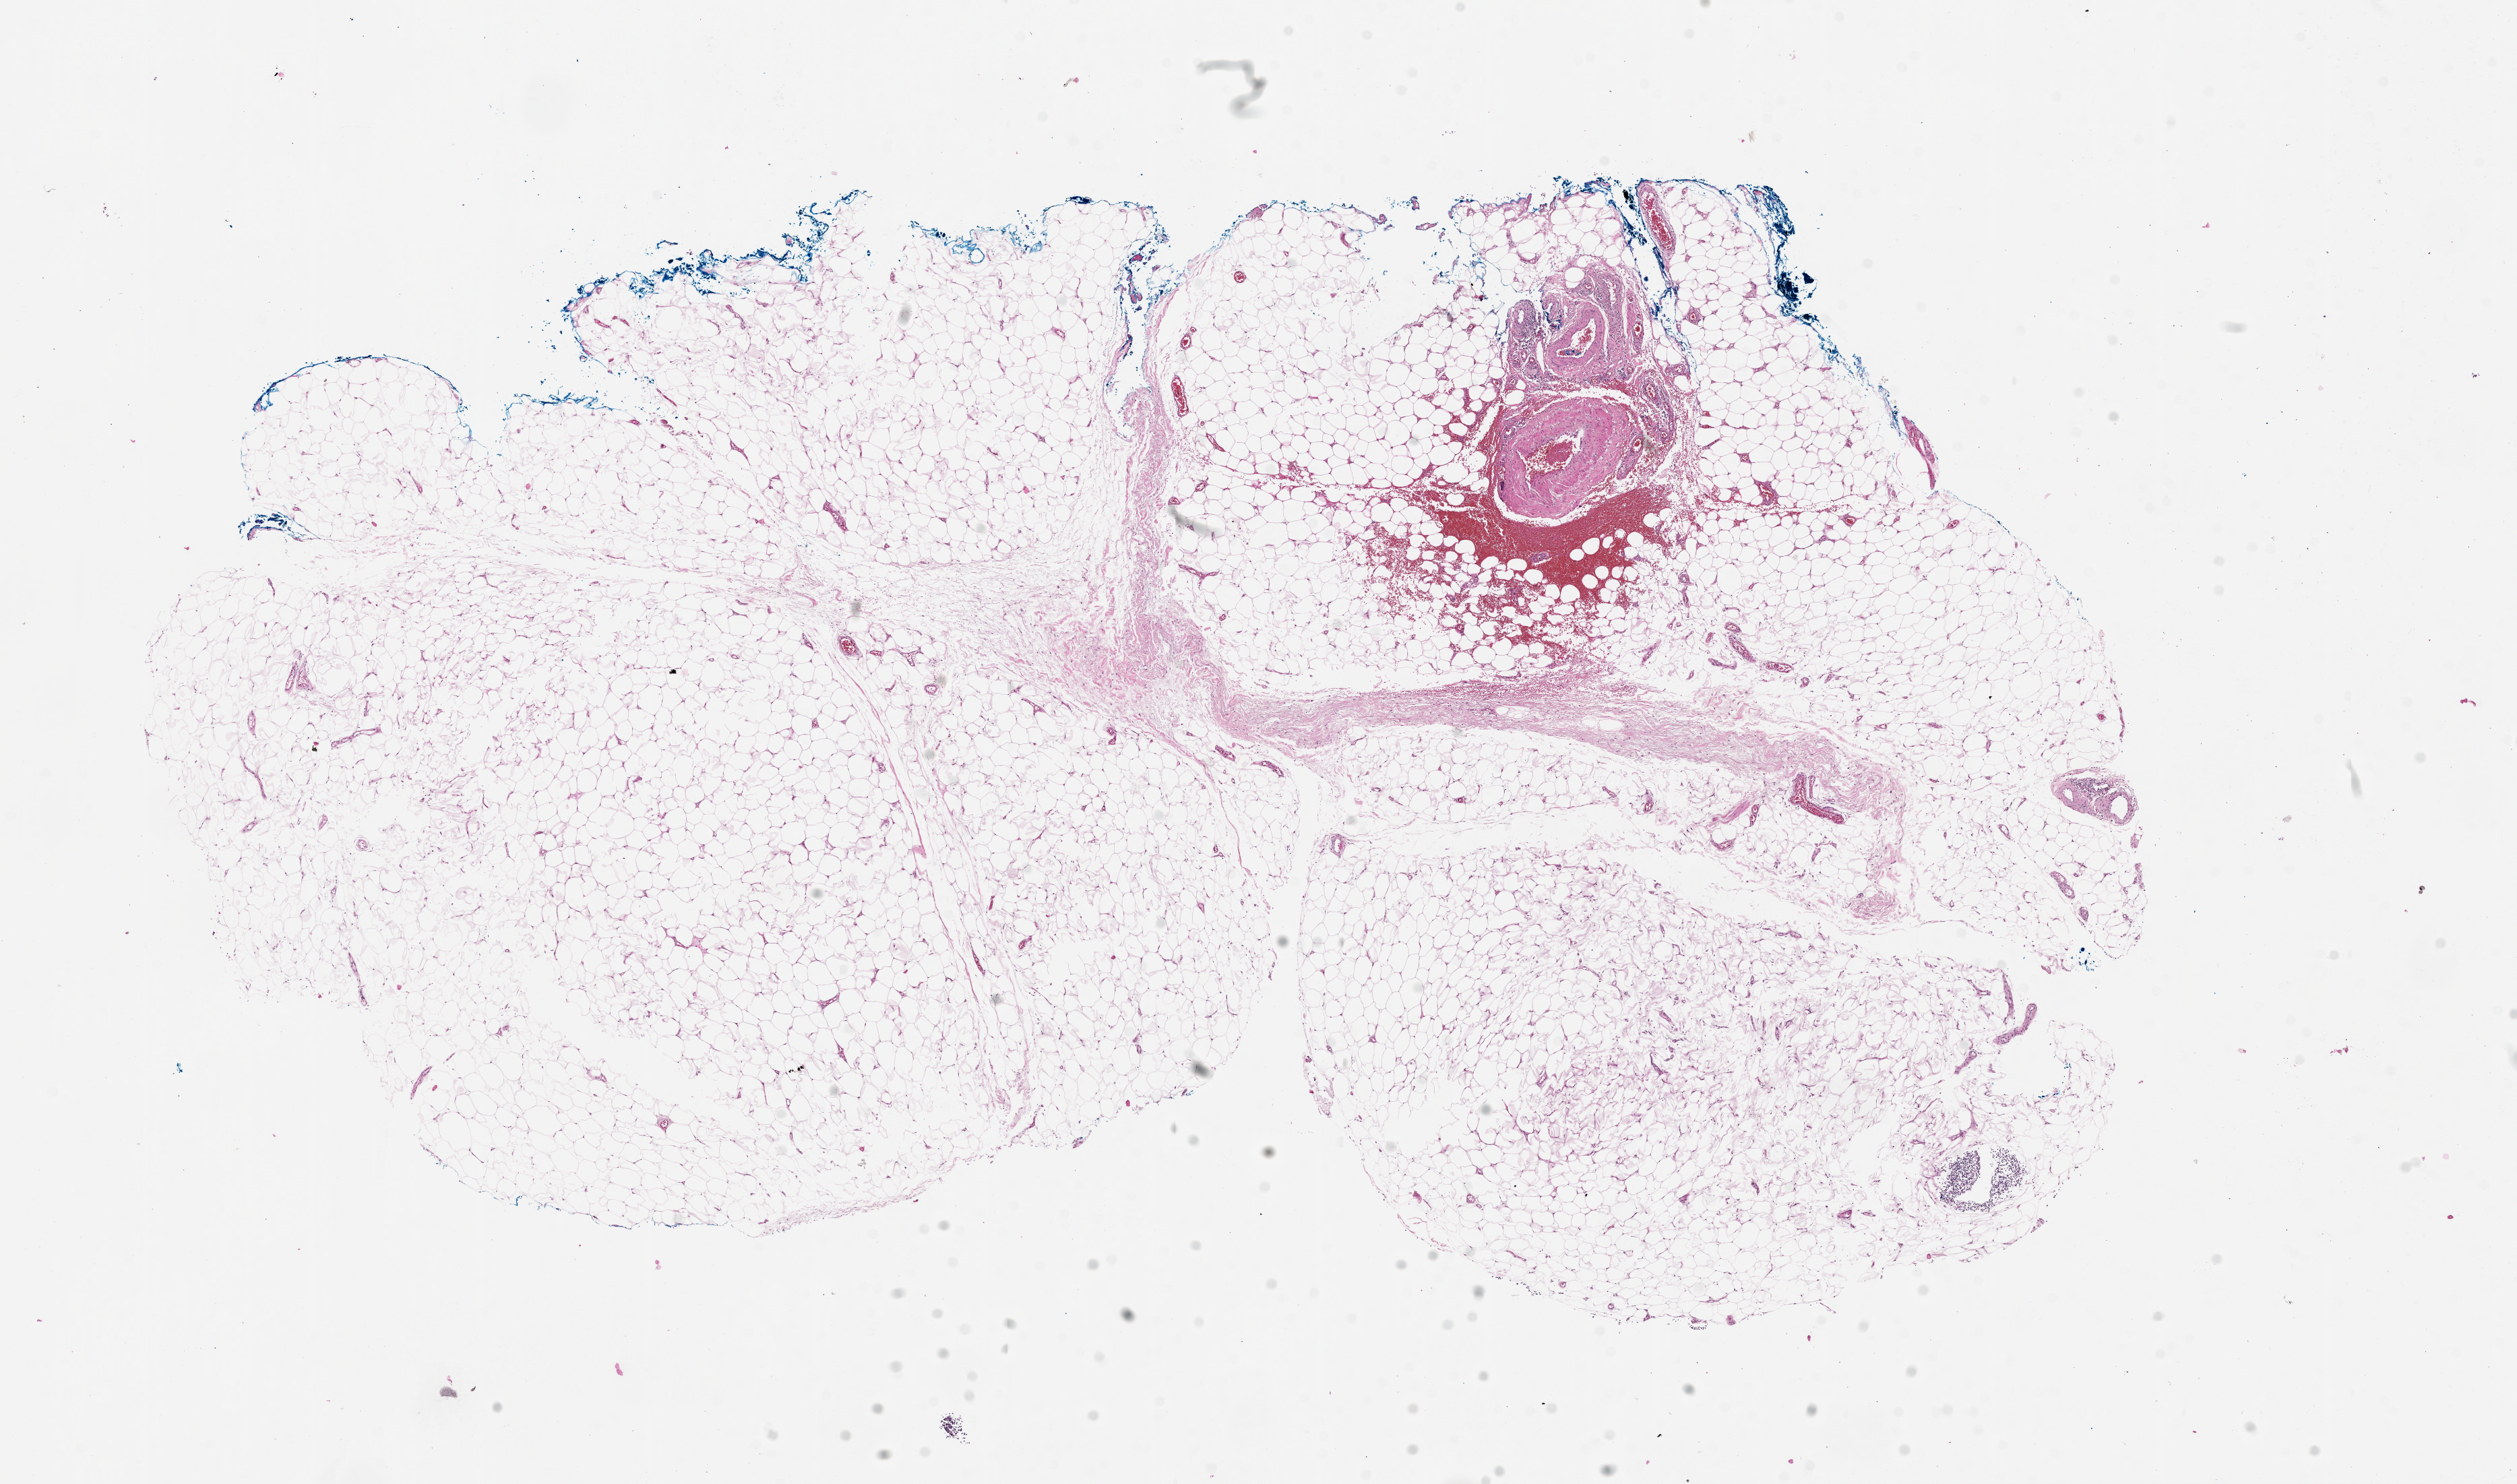
Digitized Hematoxylin and eosin (H&E) stained tissue section (whole slide) — a low-resolution overview of the entire scanned area, about 15.0 x 8.9 mm (from a 20x scan); normal (non-tumour) tissue sample, sampled site: lymph node. 54-year-old female patient.
This section: normal (non-tumour) tissue from the same patient. Patient diagnosis: Malignant melanoma, NOS.